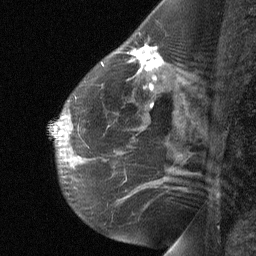
Breast MRI (dynamic contrast-enhanced), one sagittal slice. Position 39 of 64 along the scan axis. Dynamic contrast-enhanced study with each time point stored as its own series, time point 2 of 3 at this slice position (early post-contrast, ordered by acquisition time). 1.5 T. TE 4.8 ms, TR 27 ms. 2 mm slice thickness. 256 × 256 image matrix, field of view 180 × 180 mm. Female patient, age 51 years. From the clinical record (not read from this slice): setting: breast cancer imaged before/during neoadjuvant chemotherapy; receptor status: HR-positive, HER2-negative.
Structures marked on this image (semi-automatically segmented with operator editing):
- analysis volume of interest (the breast-tissue region the enhancement analysis was run in; not a lesion): bounding box (x1, y1, x2, y2) in pixels: (81, 35, 179, 103)
- tumour enhancement mask (voxels above the 90 % enhancement threshold inside the analysis volume of interest): (131, 46, 162, 69)